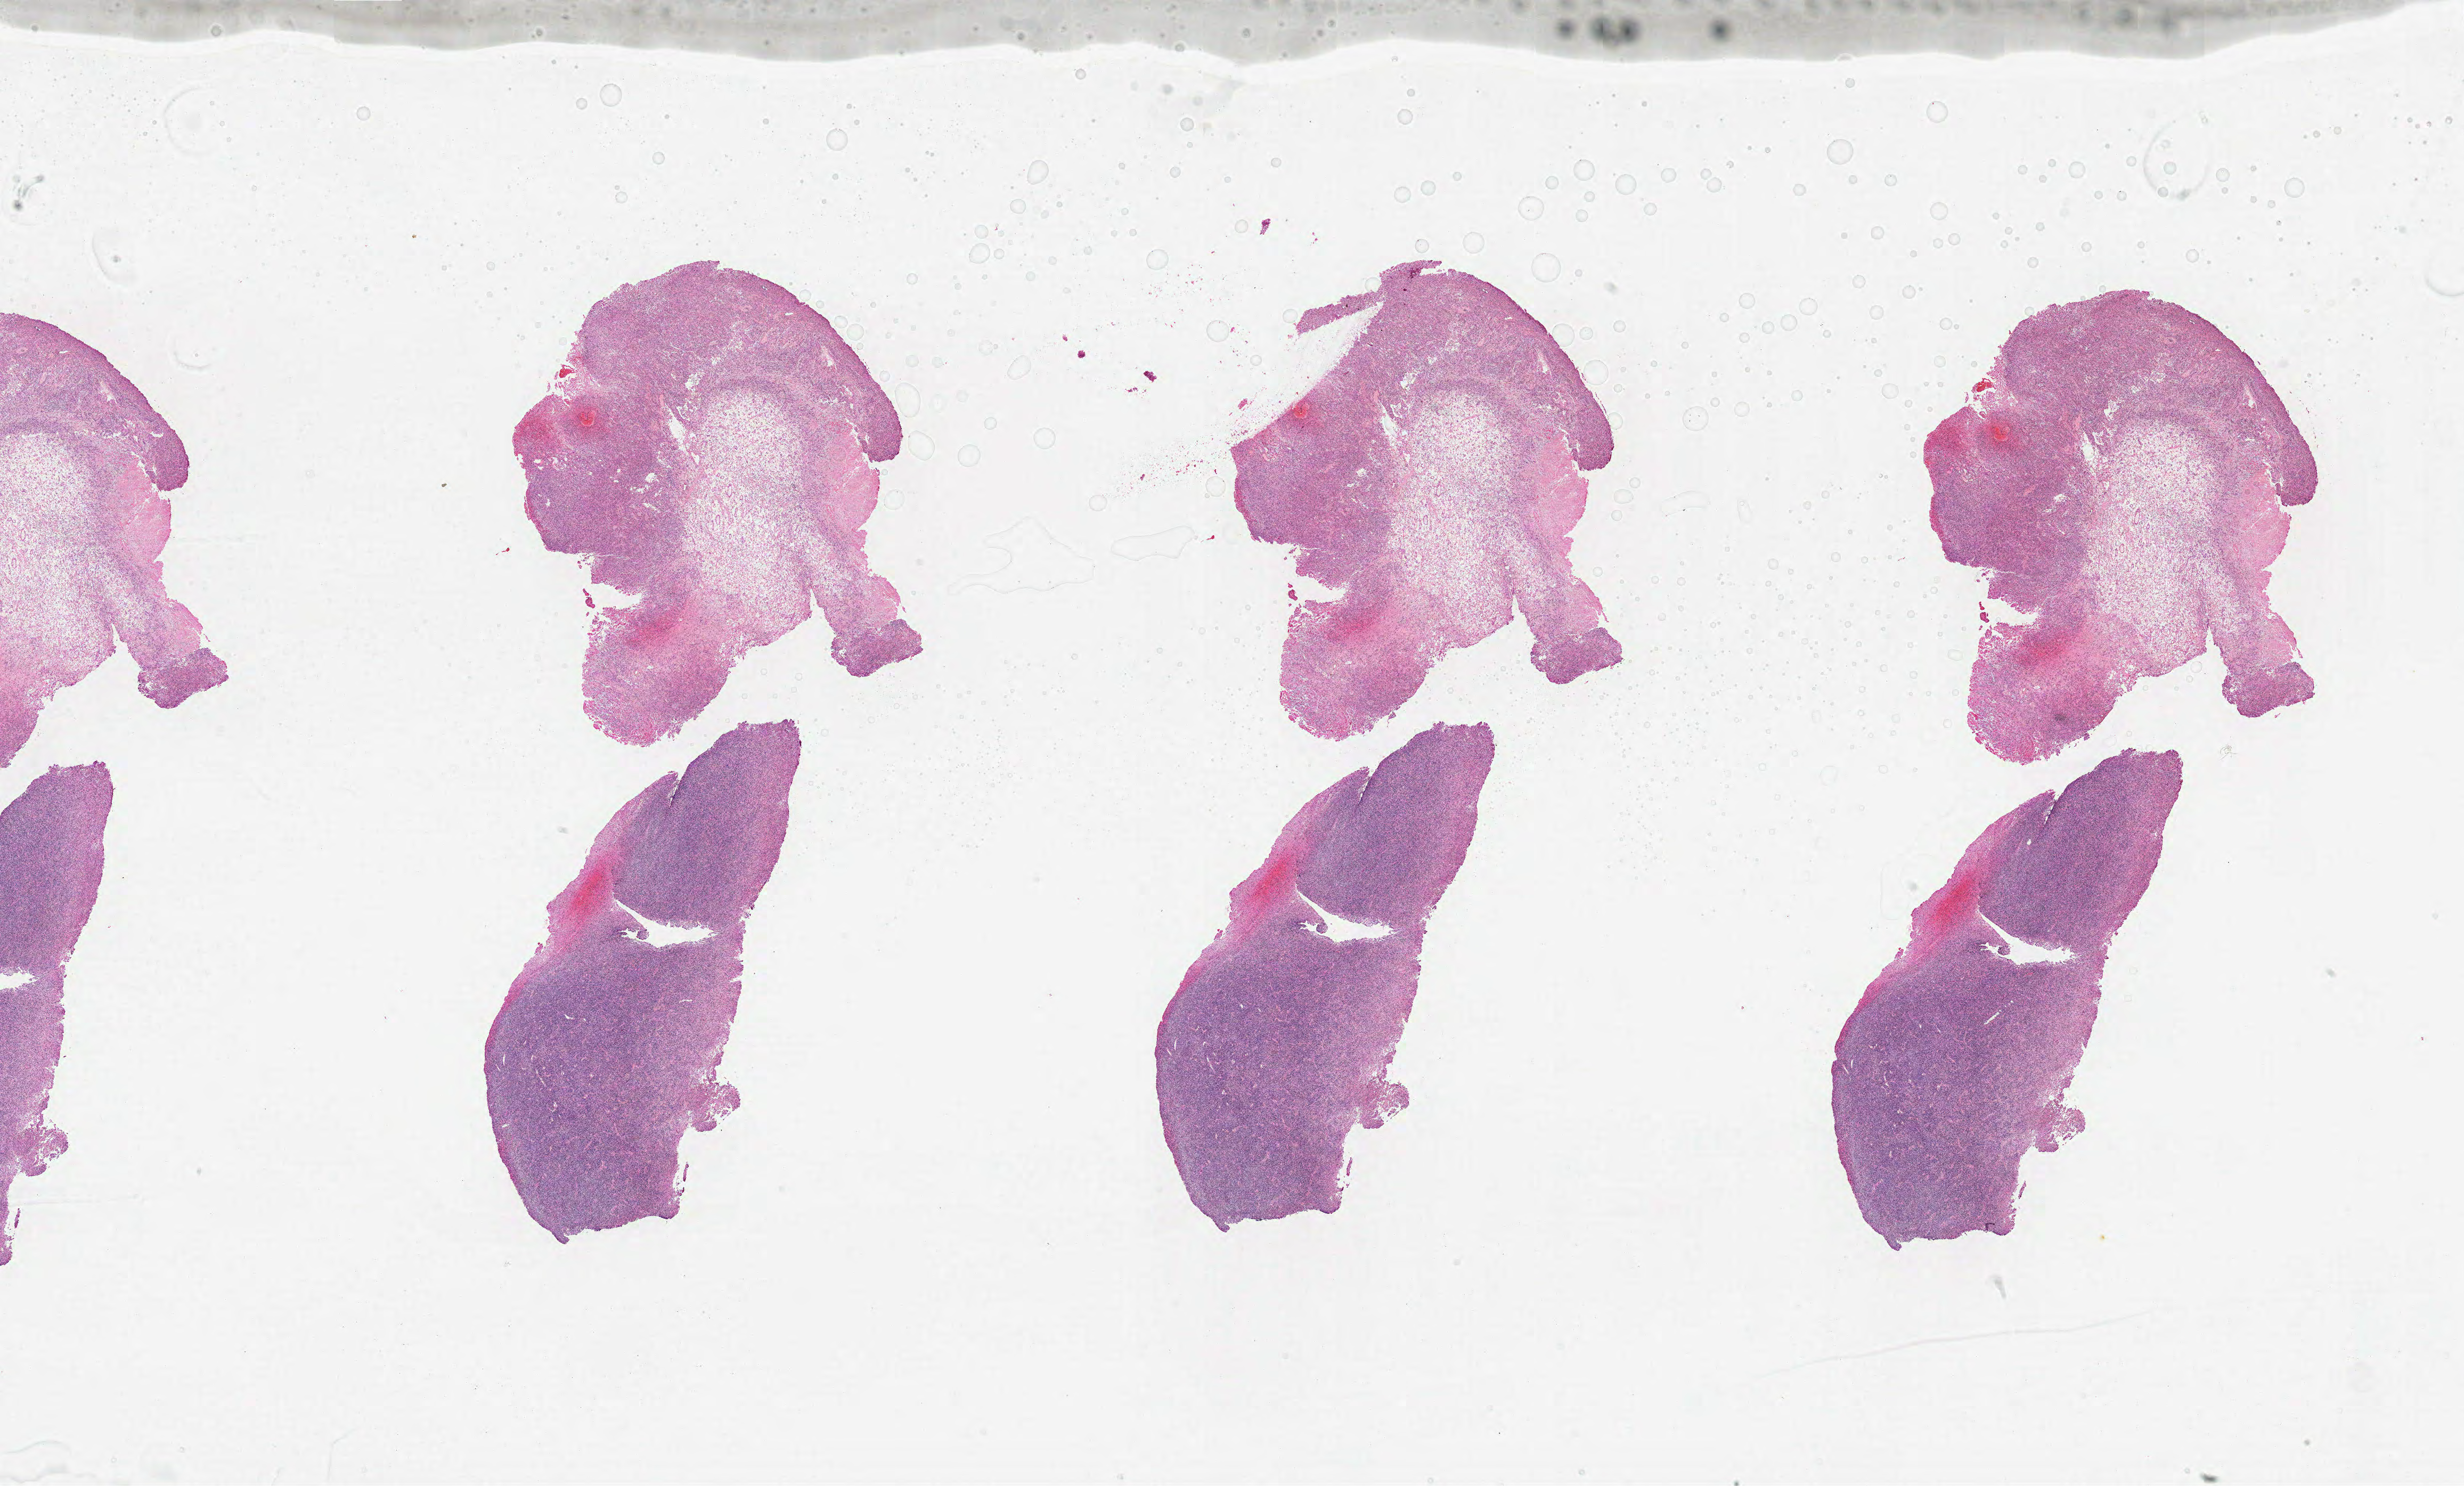
H&E whole-slide image, low-resolution overview of the scanned area, about 37.0 x 22.3 mm (from a 20x scan); FFPE section; brain, primary tumour sample. Patient: male, age at initial diagnosis 69 years.
- pathologic diagnosis: Glioblastoma